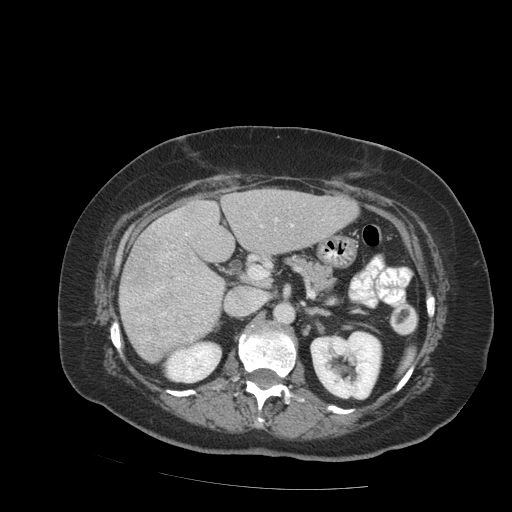
Contrast-enhanced abdominal CT (liver protocol), one axial slice; position 42 of 99 along the scan axis; soft-tissue window (W 400 / L 40 HU); 512 × 512 image matrix, field of view 400 × 400 mm. From the clinical record (not read from this slice): diagnosis: hepatocellular carcinoma (patient treated with transarterial chemoembolisation; whether this scan precedes or follows treatment is not stated here); TNM stage (as recorded): Stage-IVB; Child-Pugh class: A; tumour differentiation: moderately differentiated; tumour nodularity: uninodular.
Annotated regions visible in this slice (semi-automatically segmented with operator editing):
- liver parenchyma outside the tumour (the mass and vessels are separate outlines, so this box may not span the whole liver): bounding box (x1, y1, x2, y2) in pixels: (119, 188, 358, 362)
- mass: (121, 236, 220, 360)
- liver vessels: (175, 215, 293, 260)